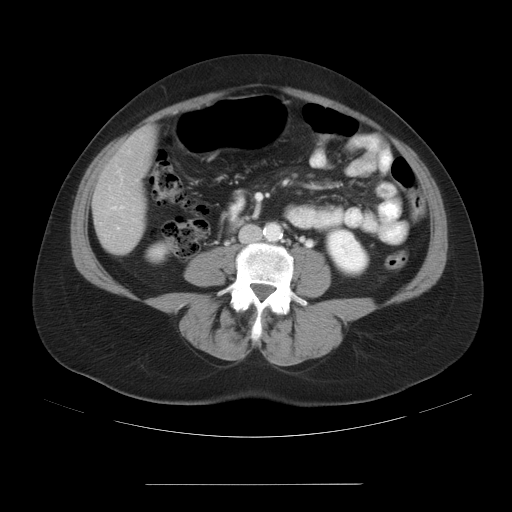
Contrast-enhanced abdominal CT, one axial slice; position 4 of 27 along the scan axis; reconstruction kernel STANDARD; 120 kVp; intravenous contrast given; soft-tissue window (W 400 / L 40 HU); 7.5 mm slice thickness; 512 × 512 image matrix, field of view 440 × 440 mm. Female patient, age 58 years. From the clinical record (not read from this slice): diagnosis: colorectal cancer liver metastases, imaged before liver resection; multiple liver metastases: yes; largest metastasis: 1.9 cm; disease in both lobes: yes.
Structures marked on this image (manually delineated by an expert):
- liver: bounding box (x1, y1, x2, y2) in pixels: (94, 131, 153, 254)
- planned liver remnant (the part of the liver to remain after resection): (104, 131, 154, 184)
- portal vein (with intrahepatic branches): (116, 168, 123, 188)